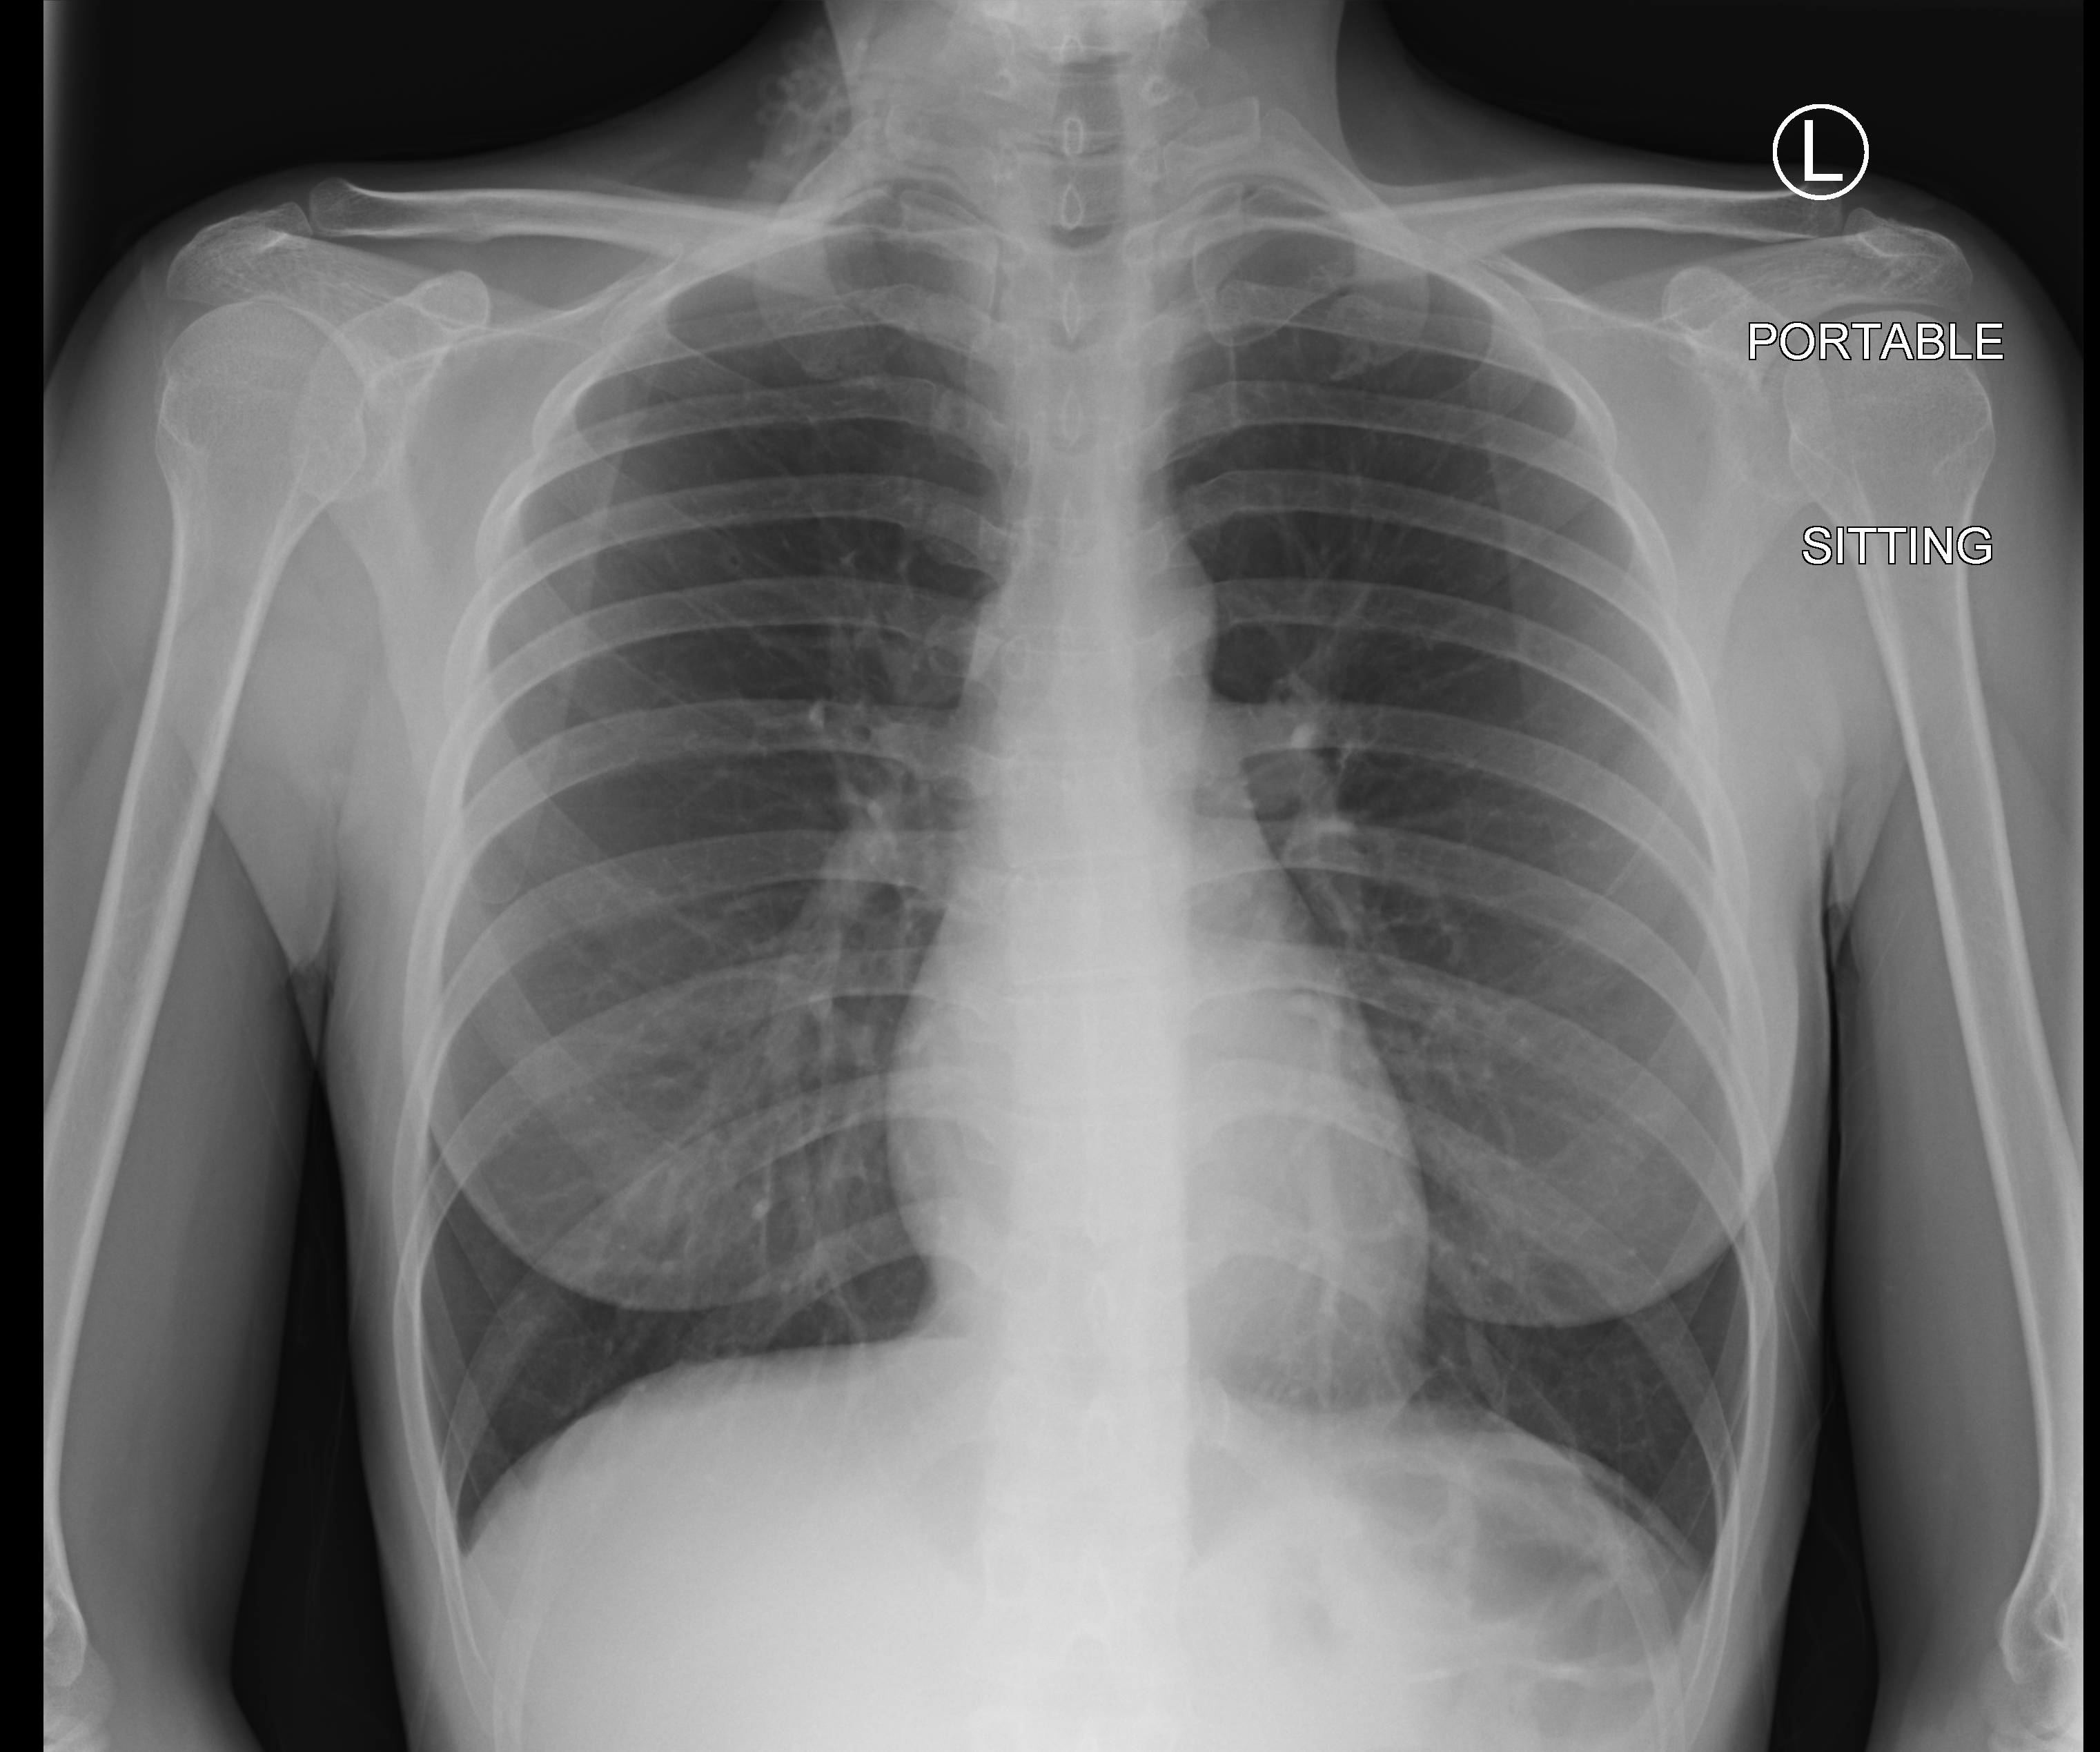
Chest X-ray (portable), anteroposterior (AP) projection. Female patient hospitalised with COVID-19, age 18–59 years.
Hospital-stay facts (about this admission, not read from this image; timing relative to this image not recorded): admitted to intensive care during this hospital stay: no; mechanically ventilated during this hospital stay: no.